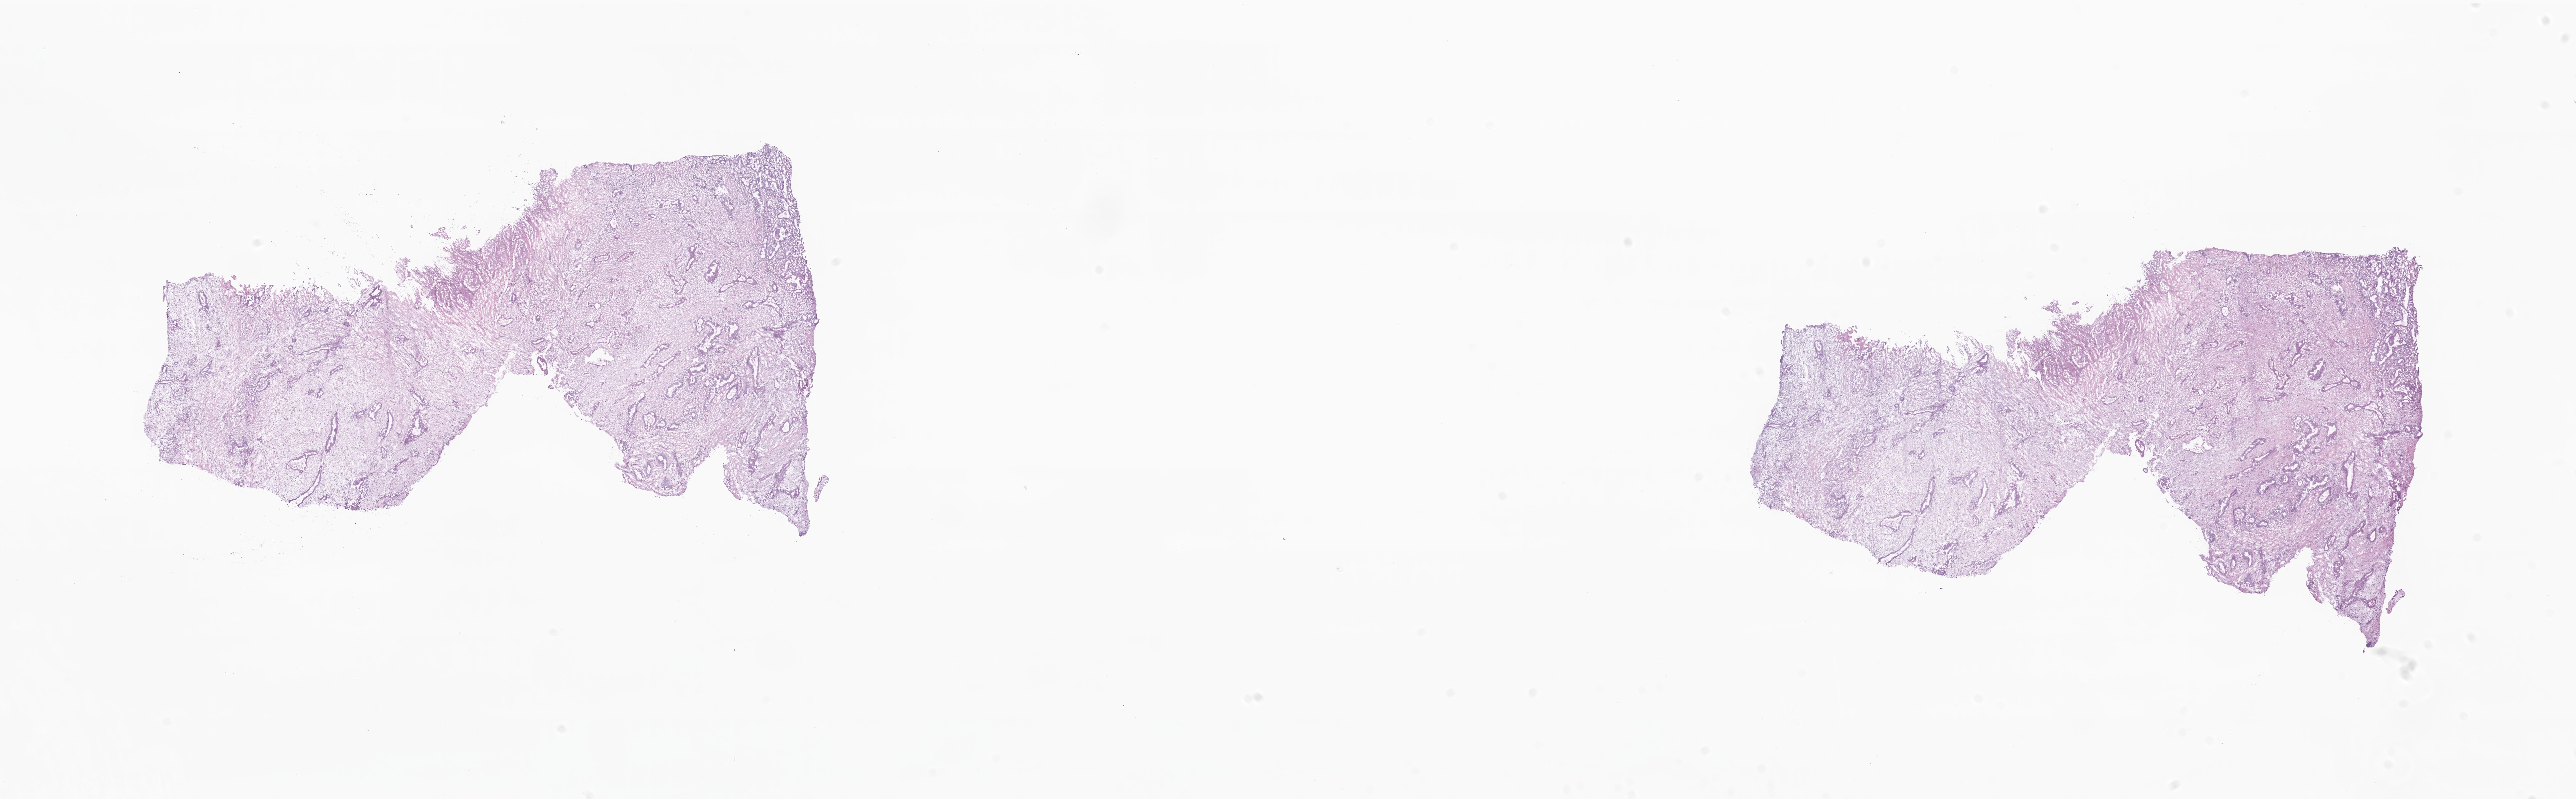
Whole-slide image, hematoxylin and eosin (H&E) stain — whole scanned area (about 32.7 x 10.1 mm) shown as a low-resolution overview, cryosection, primary tumor, anatomic site: tail of pancreas. Male, age 68 years at initial diagnosis. Pathologist review of this section (percent, as recorded): tumor cells 20%, tumor nuclei 25%, stromal cells 80%, necrosis 0%, normal cells 0%. Infiltration values recorded for this section: lymphocyte infiltration 0%, monocyte infiltration 0%, neutrophil infiltration 0%.
Diagnosis: Infiltrating duct carcinoma, NOS. Section: bottom of the tissue portion.